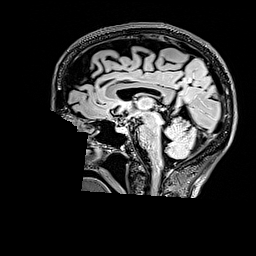
Brain MRI from a brain-tumour surgery series, one sagittal slice. Slice 93 of 176 in the series (ordered by position). T2 FLAIR. 1 mm slice thickness. 256 × 256 image matrix, field of view 256 × 256 mm. Case-level facts recorded for this patient, not image findings: histopathology: Astrocytoma; WHO grade: 3.
Structures marked on this image (manually delineated by an expert):
- tumour: box from (x=185, y=58) to (x=205, y=72) px
- tumour: (x=186, y=59)–(x=205, y=76)